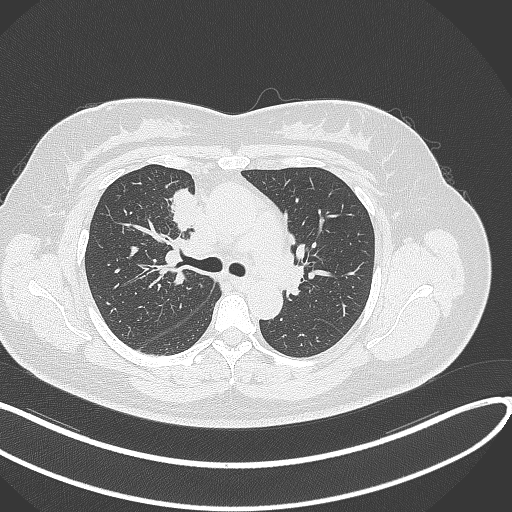
Chest CT, one axial slice. Position 181 of 303 along the scan axis. Reconstruction kernel B70f. Lung window (W 1500 / L -600 HU). 1 mm slice thickness. 512 × 512 image matrix. Patient: female, 46 years. From the clinical record (not read from this slice): clinical TNM (as recorded): T2a N1 M0.
Structures marked on this image (bounding box drawn by a radiologist):
- lung tumour (recorded histology: adenocarcinoma): bounding box <168,186,204,236> (left, top, right, bottom; pixels)